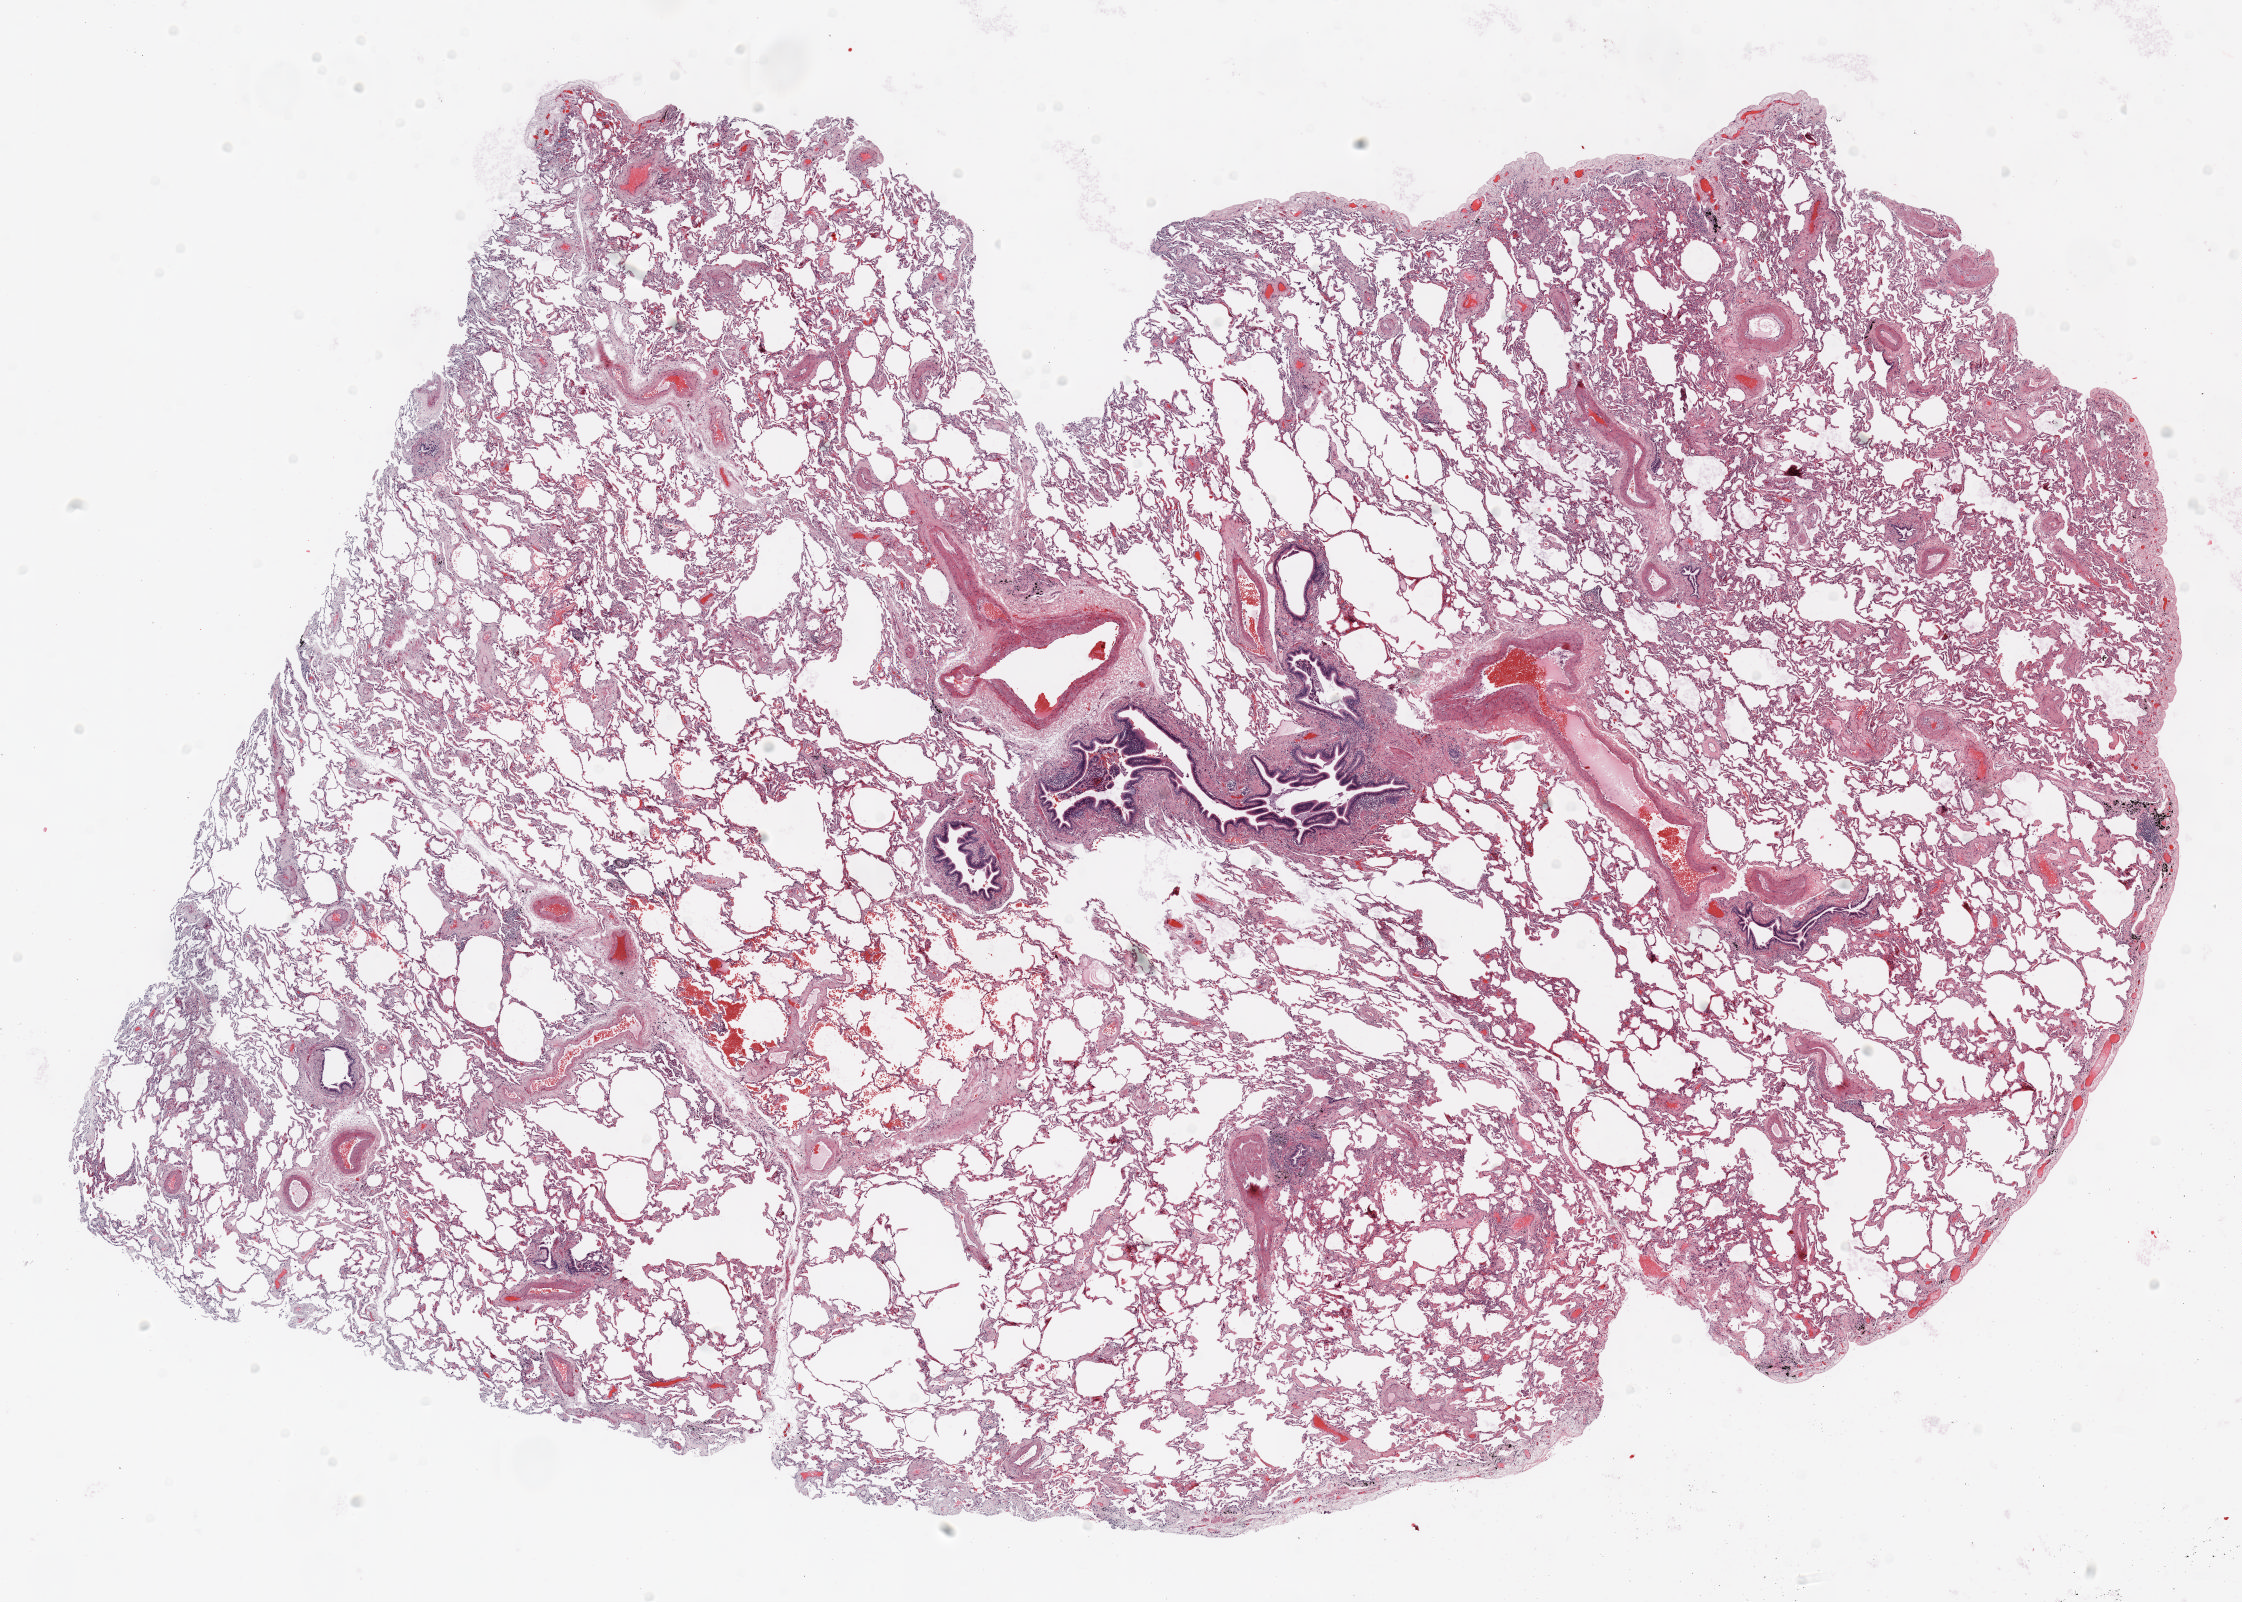
Hematoxylin and eosin (H&E) stained whole-slide image, low-resolution overview of the scanned area, about 18.0 x 12.9 mm (from a 20x scan). Formalin-fixed paraffin-embedded (FFPE) section. Lung. Female, age 72 at enrolment. Grade: moderately differentiated (G2).
• ICD-O-3 topography: upper lobe of lung (C34.1)
• participant's lung-cancer diagnosis: Adenocarcinoma, NOS
• tumour size (pathology): 15 mm
• stage (AJCC 6th edition): IA
• primary tumour location (clinical record): right upper lobe